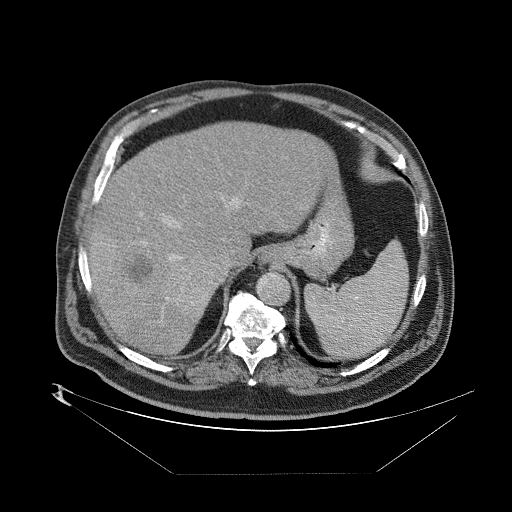
Contrast-enhanced abdominal CT (liver protocol), one axial slice. Position 61 of 89 along the scan axis. Reconstruction kernel STANDARD. One of 2 acquisitions stored at this slice position. Soft-tissue window (W 400 / L 40 HU). 2.5 mm slice thickness. 512 × 512 image matrix. From the clinical record (not read from this slice): diagnosis: hepatocellular carcinoma (patient treated with transarterial chemoembolisation; whether this scan precedes or follows treatment is not stated here); TNM stage (as recorded): Stage-II; Child-Pugh class: B; tumour differentiation: moderately differentiated; tumour nodularity: multinodular.
Structures marked on this image (semi-automatically segmented with operator editing):
- abdominal aorta: bounding box <257,273,290,306> (left, top, right, bottom; pixels)
- liver parenchyma outside the tumour (the mass and vessels are separate outlines, so this box may not span the whole liver): <88,118,348,354>
- mass: <91,235,219,318>
- liver vessels: <90,194,344,322>